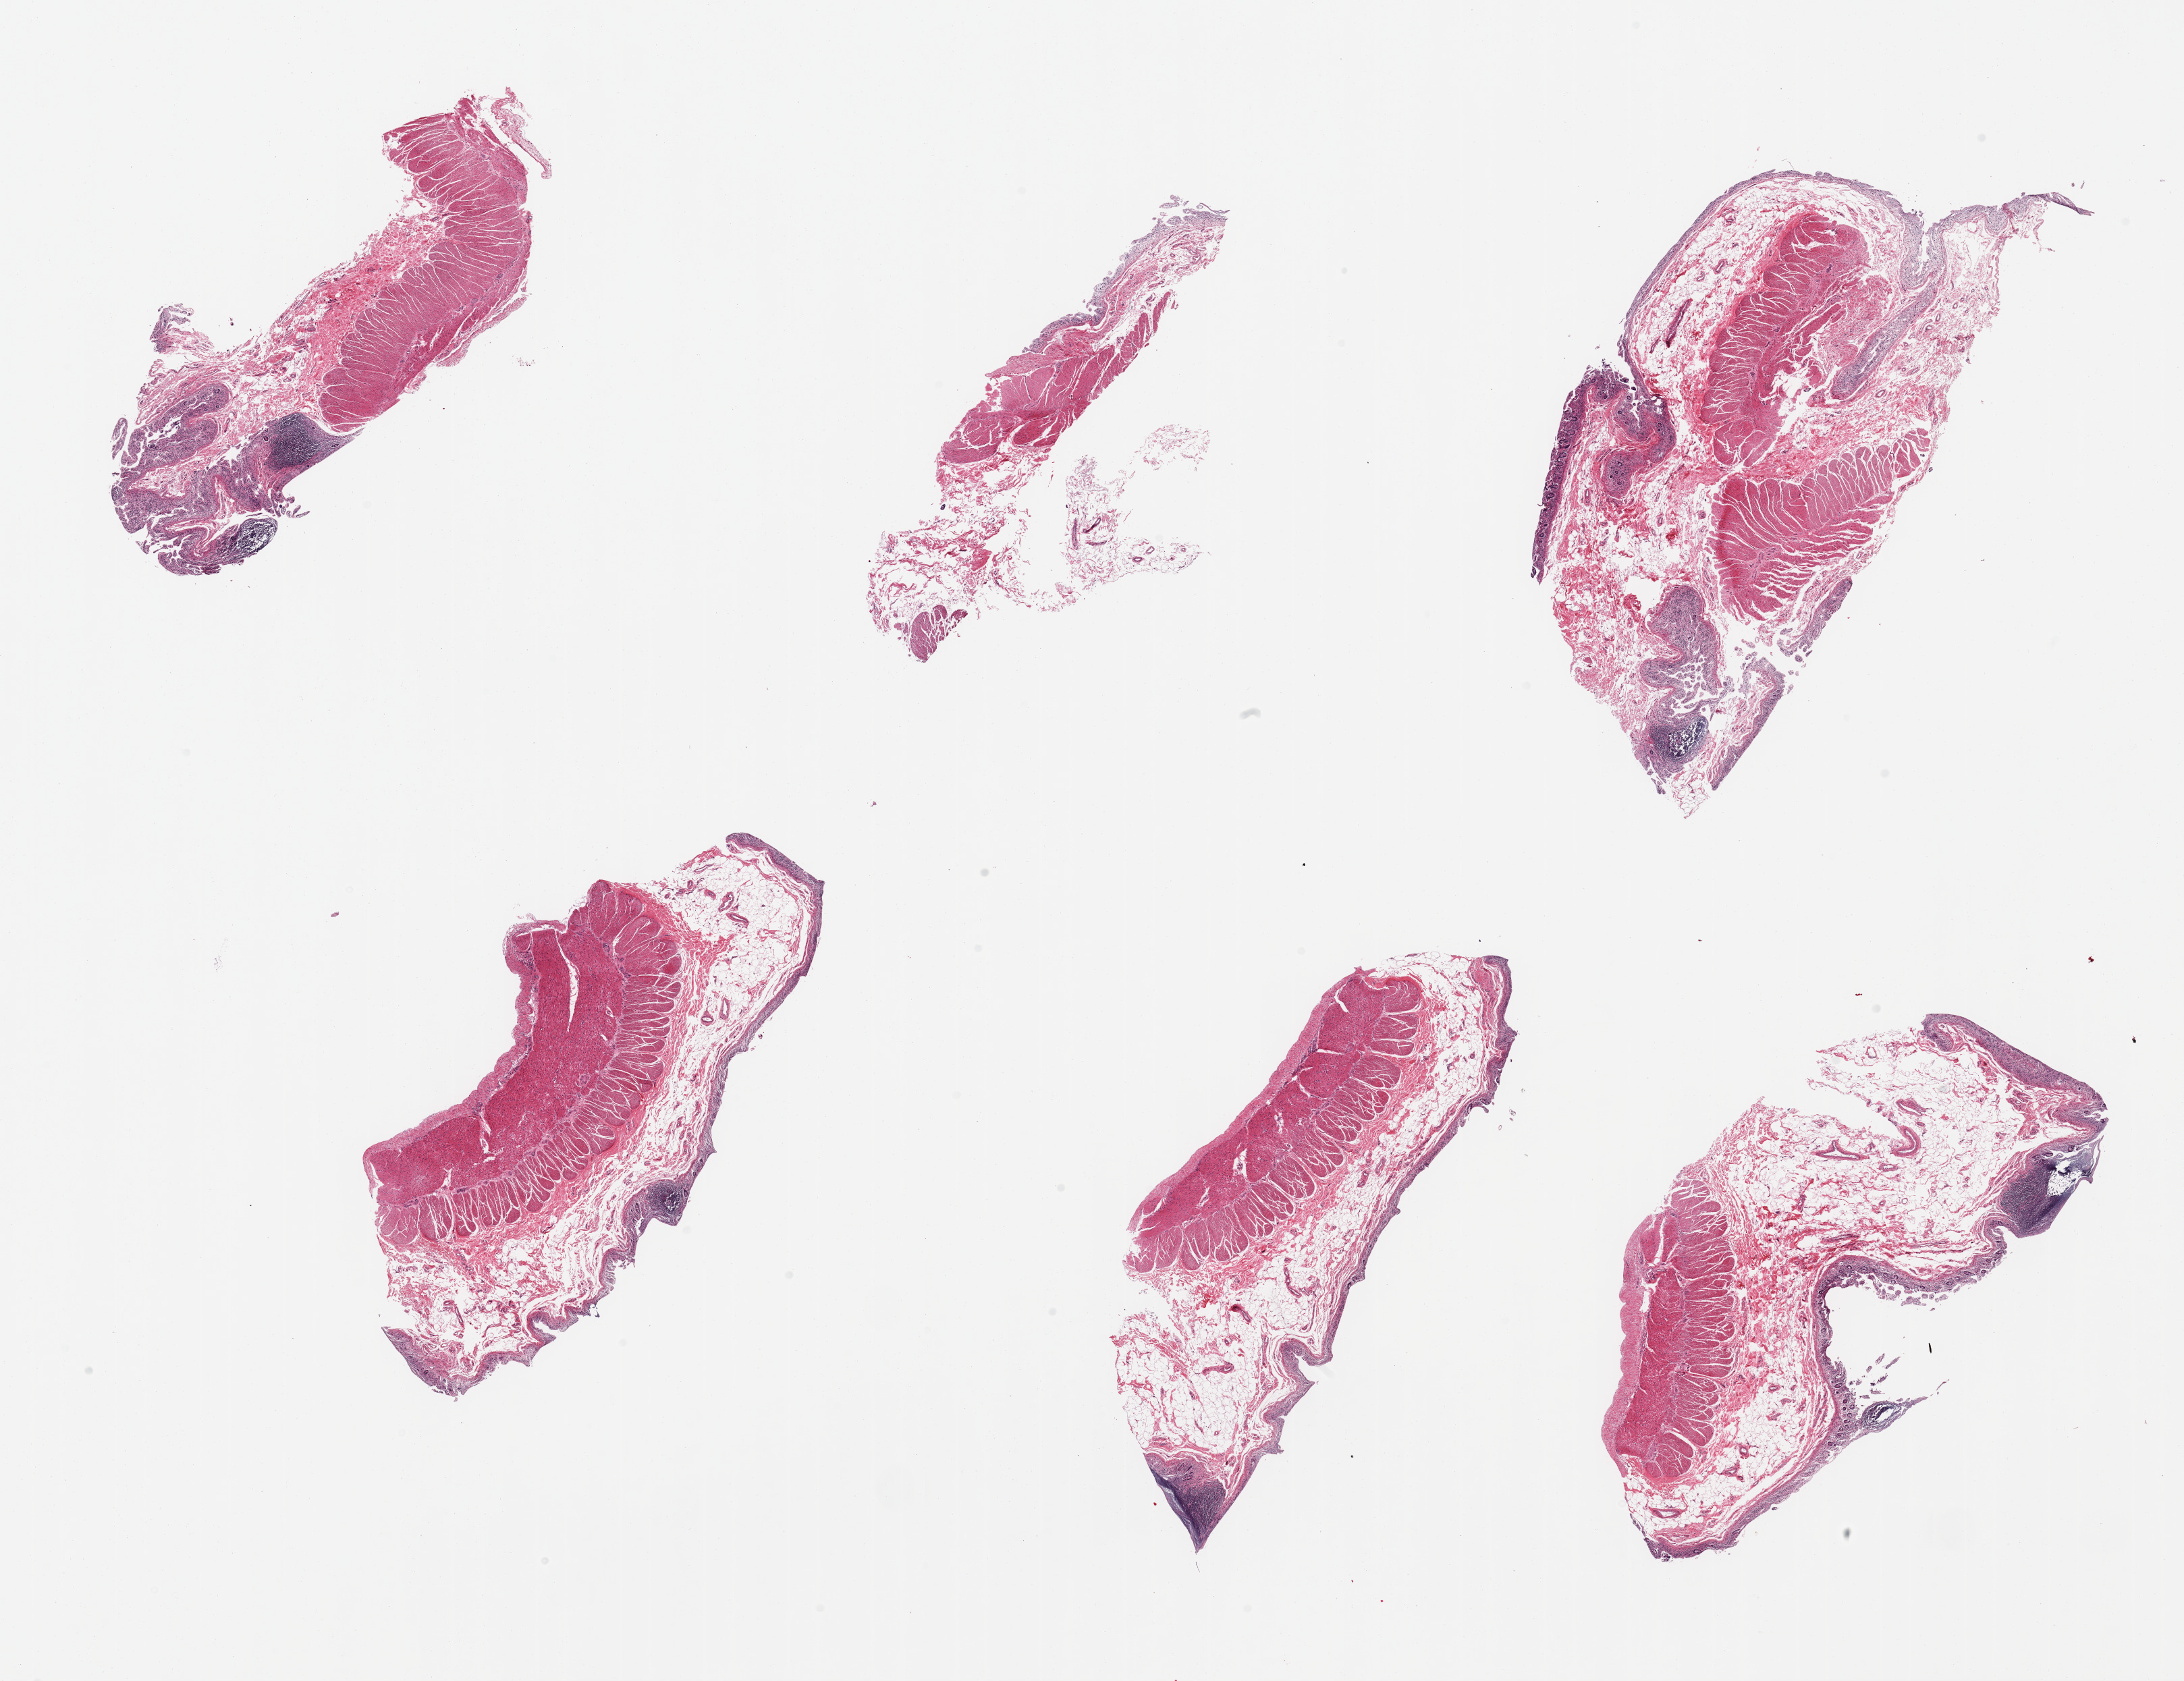
Hematoxylin and eosin (H&E) whole-slide image, low-resolution overview of the scanned area, about 25.6 x 19.7 mm. Donor sex: male.
* specimen: PAXgene-fixed, paraffin-embedded tissue; target tissue: ileum; tissue donor sample